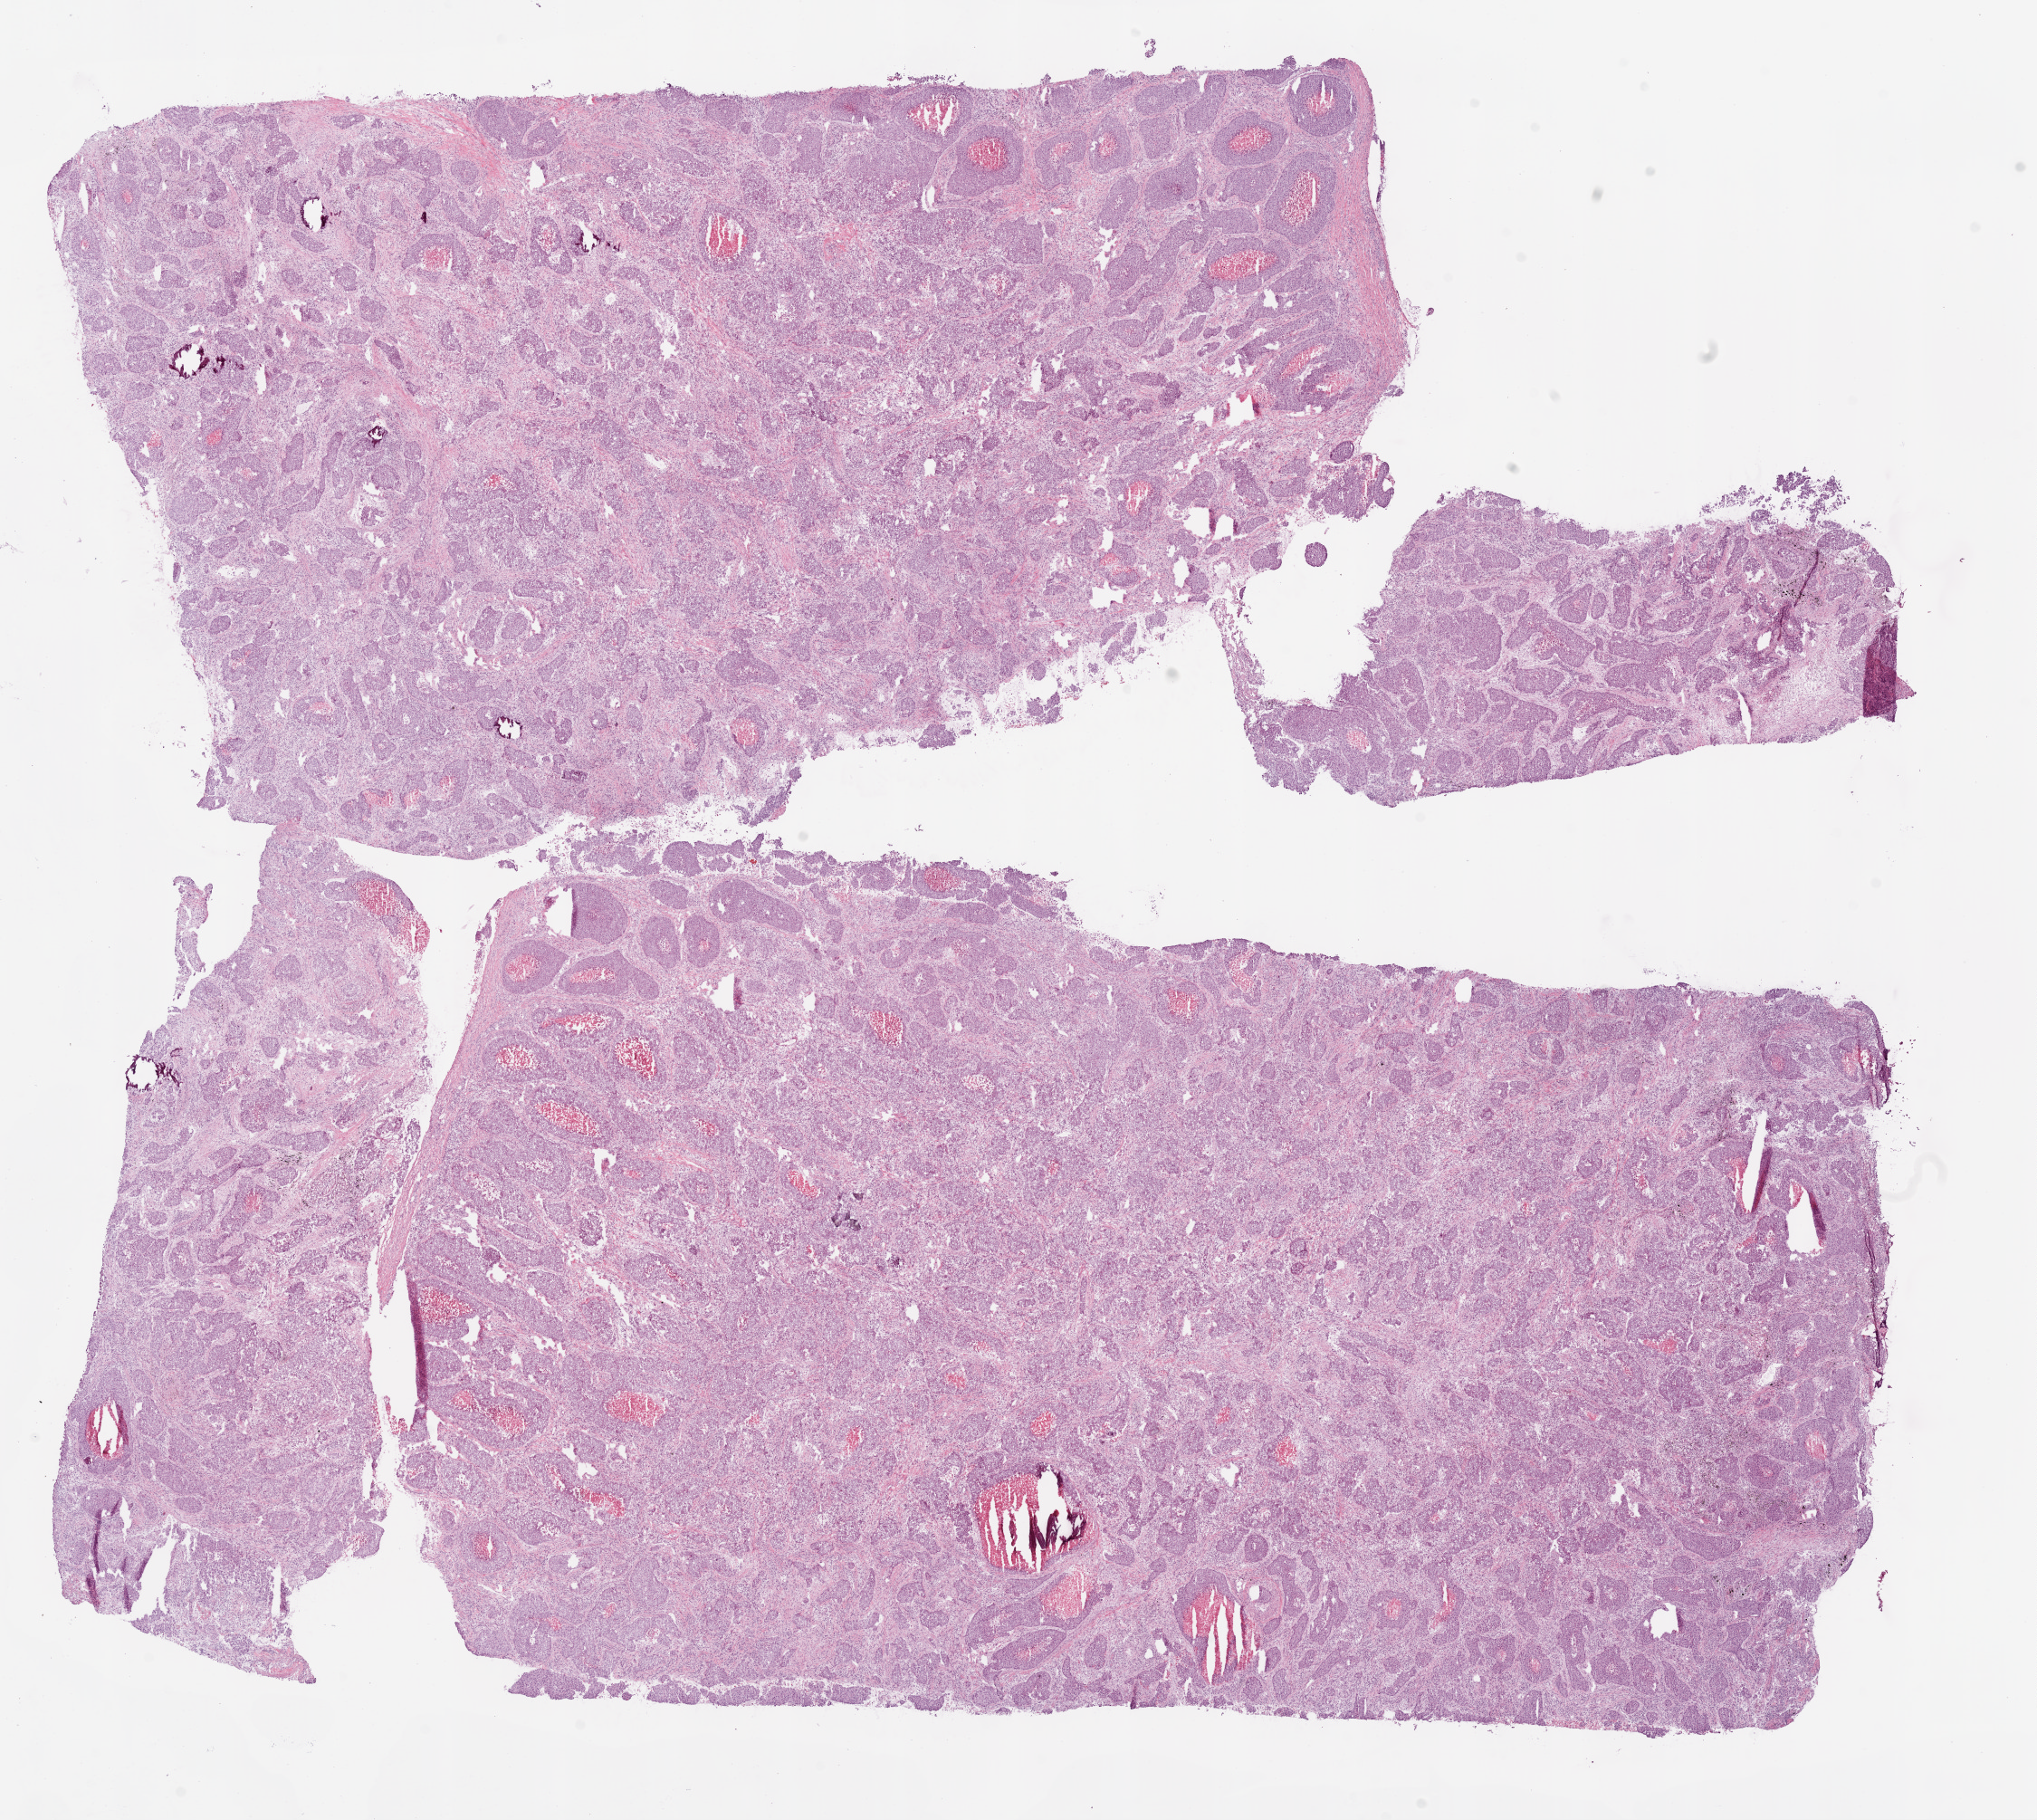
H&E-stained whole-slide image — whole scanned area (about 18.1 x 16.1 mm) shown as a low-resolution overview, frozen section from the top of the tissue portion, lung, primary tumour sample. Female patient; age at initial diagnosis 73 years. Pathologist review of this section (percent, as recorded): tumour cells 60%, tumour nuclei 65%, normal cells 0%, stromal cells 30%, necrosis 10%.
TNM: T3 N0 M0. AJCC pathologic stage: IIB. Histologic diagnosis: Squamous cell carcinoma, NOS.